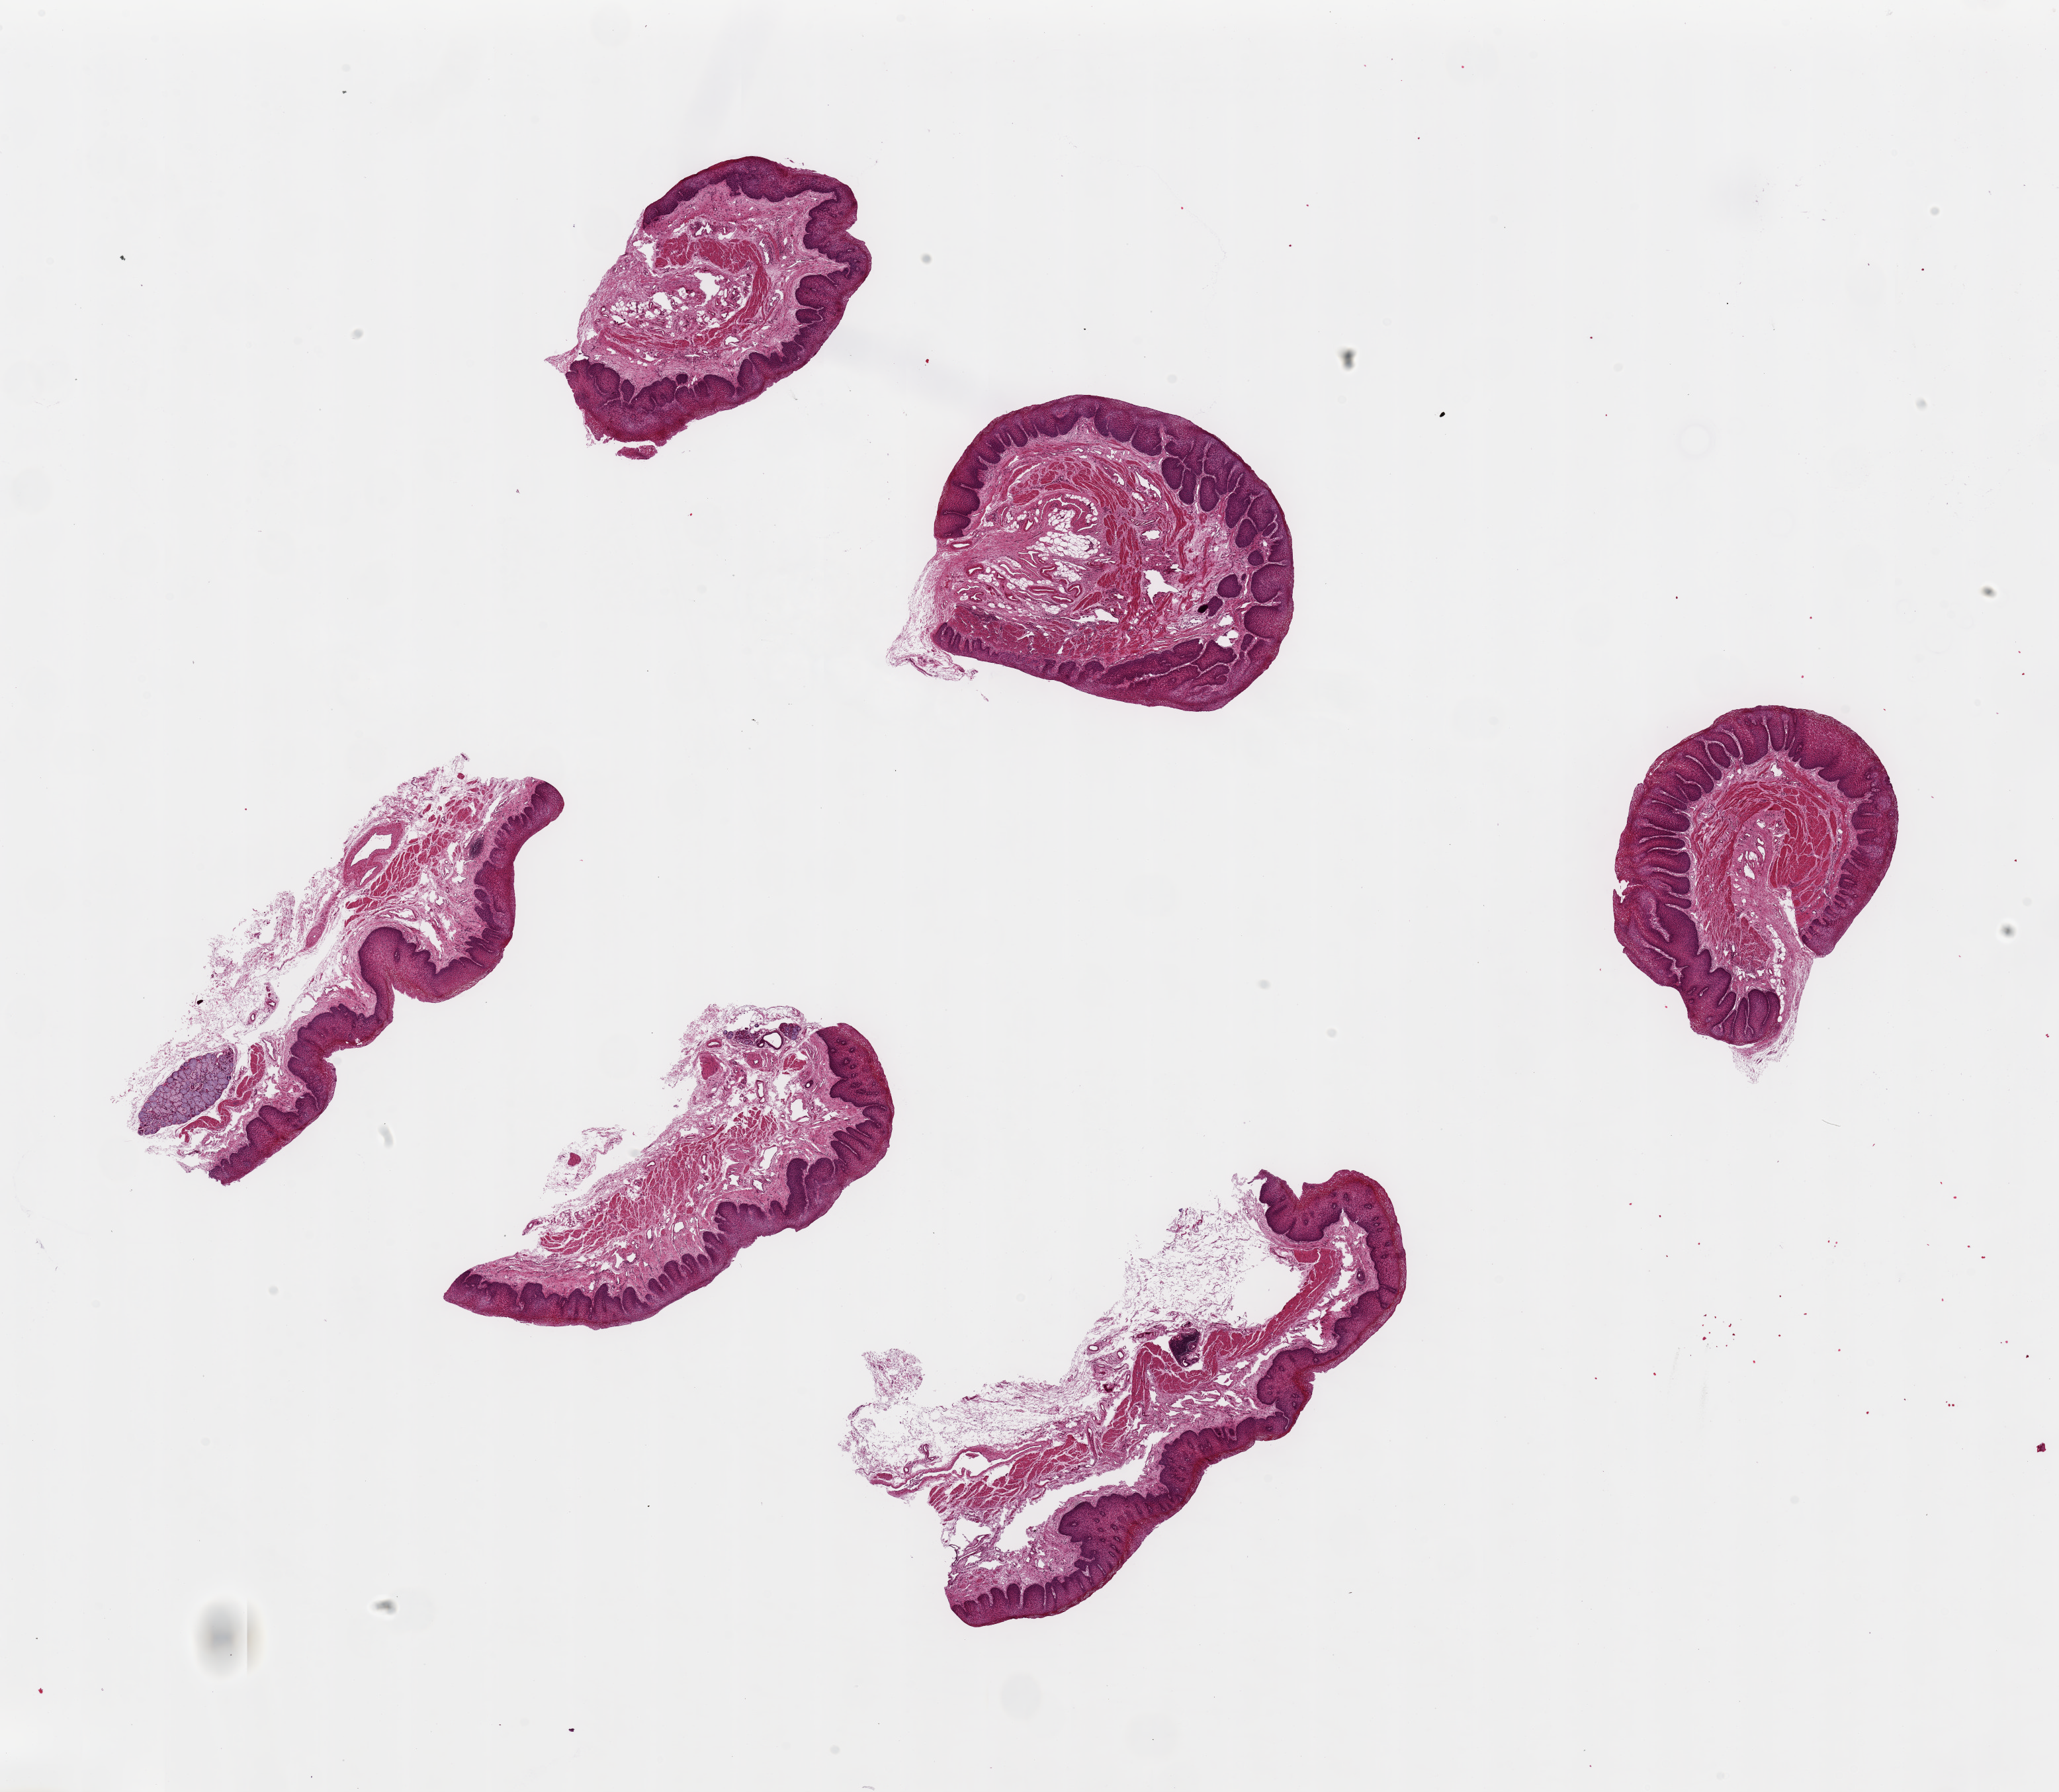
Haematoxylin and eosin whole-slide image, low-resolution overview of the scanned area, about 24.6 x 21.4 mm (from a 20x scan). PAXgene-fixed paraffin-embedded (PFPE) section. Section of esophageal mucous membrane (target tissue). Tissue donor sample. Donor: male.
Review note (as recorded): 6 pieces up to 7x2.5 mm; hyperplastic mucosa up to 0.7mm.